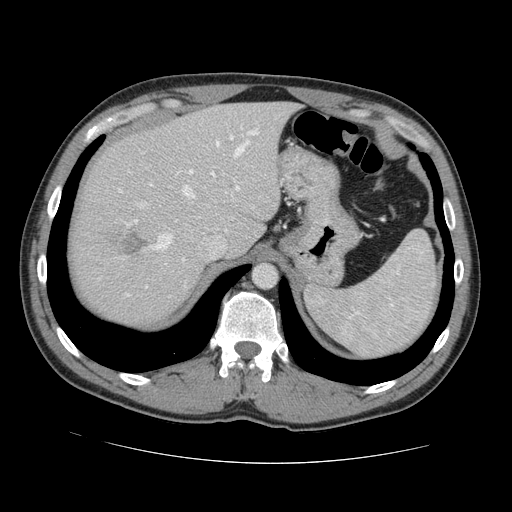
Contrast-enhanced abdominal CT, one axial slice; position 104 of 131 along the scan axis; 120 kVp; intravenous contrast given; soft-tissue window (W 400 / L 40 HU); 2.5 mm slice thickness; 512 × 512 image matrix. Male patient, age 40 years. From the clinical record (not read from this slice): diagnosis: colorectal cancer liver metastases, imaged before liver resection; multiple liver metastases: yes; largest metastasis: 2.9 cm.
Outlined on this slice (manually delineated by an expert):
- hepatic veins: bounding box (x1, y1, x2, y2) in pixels: (154, 141, 249, 250)
- liver: (73, 103, 292, 323)
- planned liver remnant (the part of the liver to remain after resection): (99, 102, 293, 256)
- portal vein (with intrahepatic branches): (189, 132, 258, 191)
- liver metastasis: (112, 231, 147, 256)